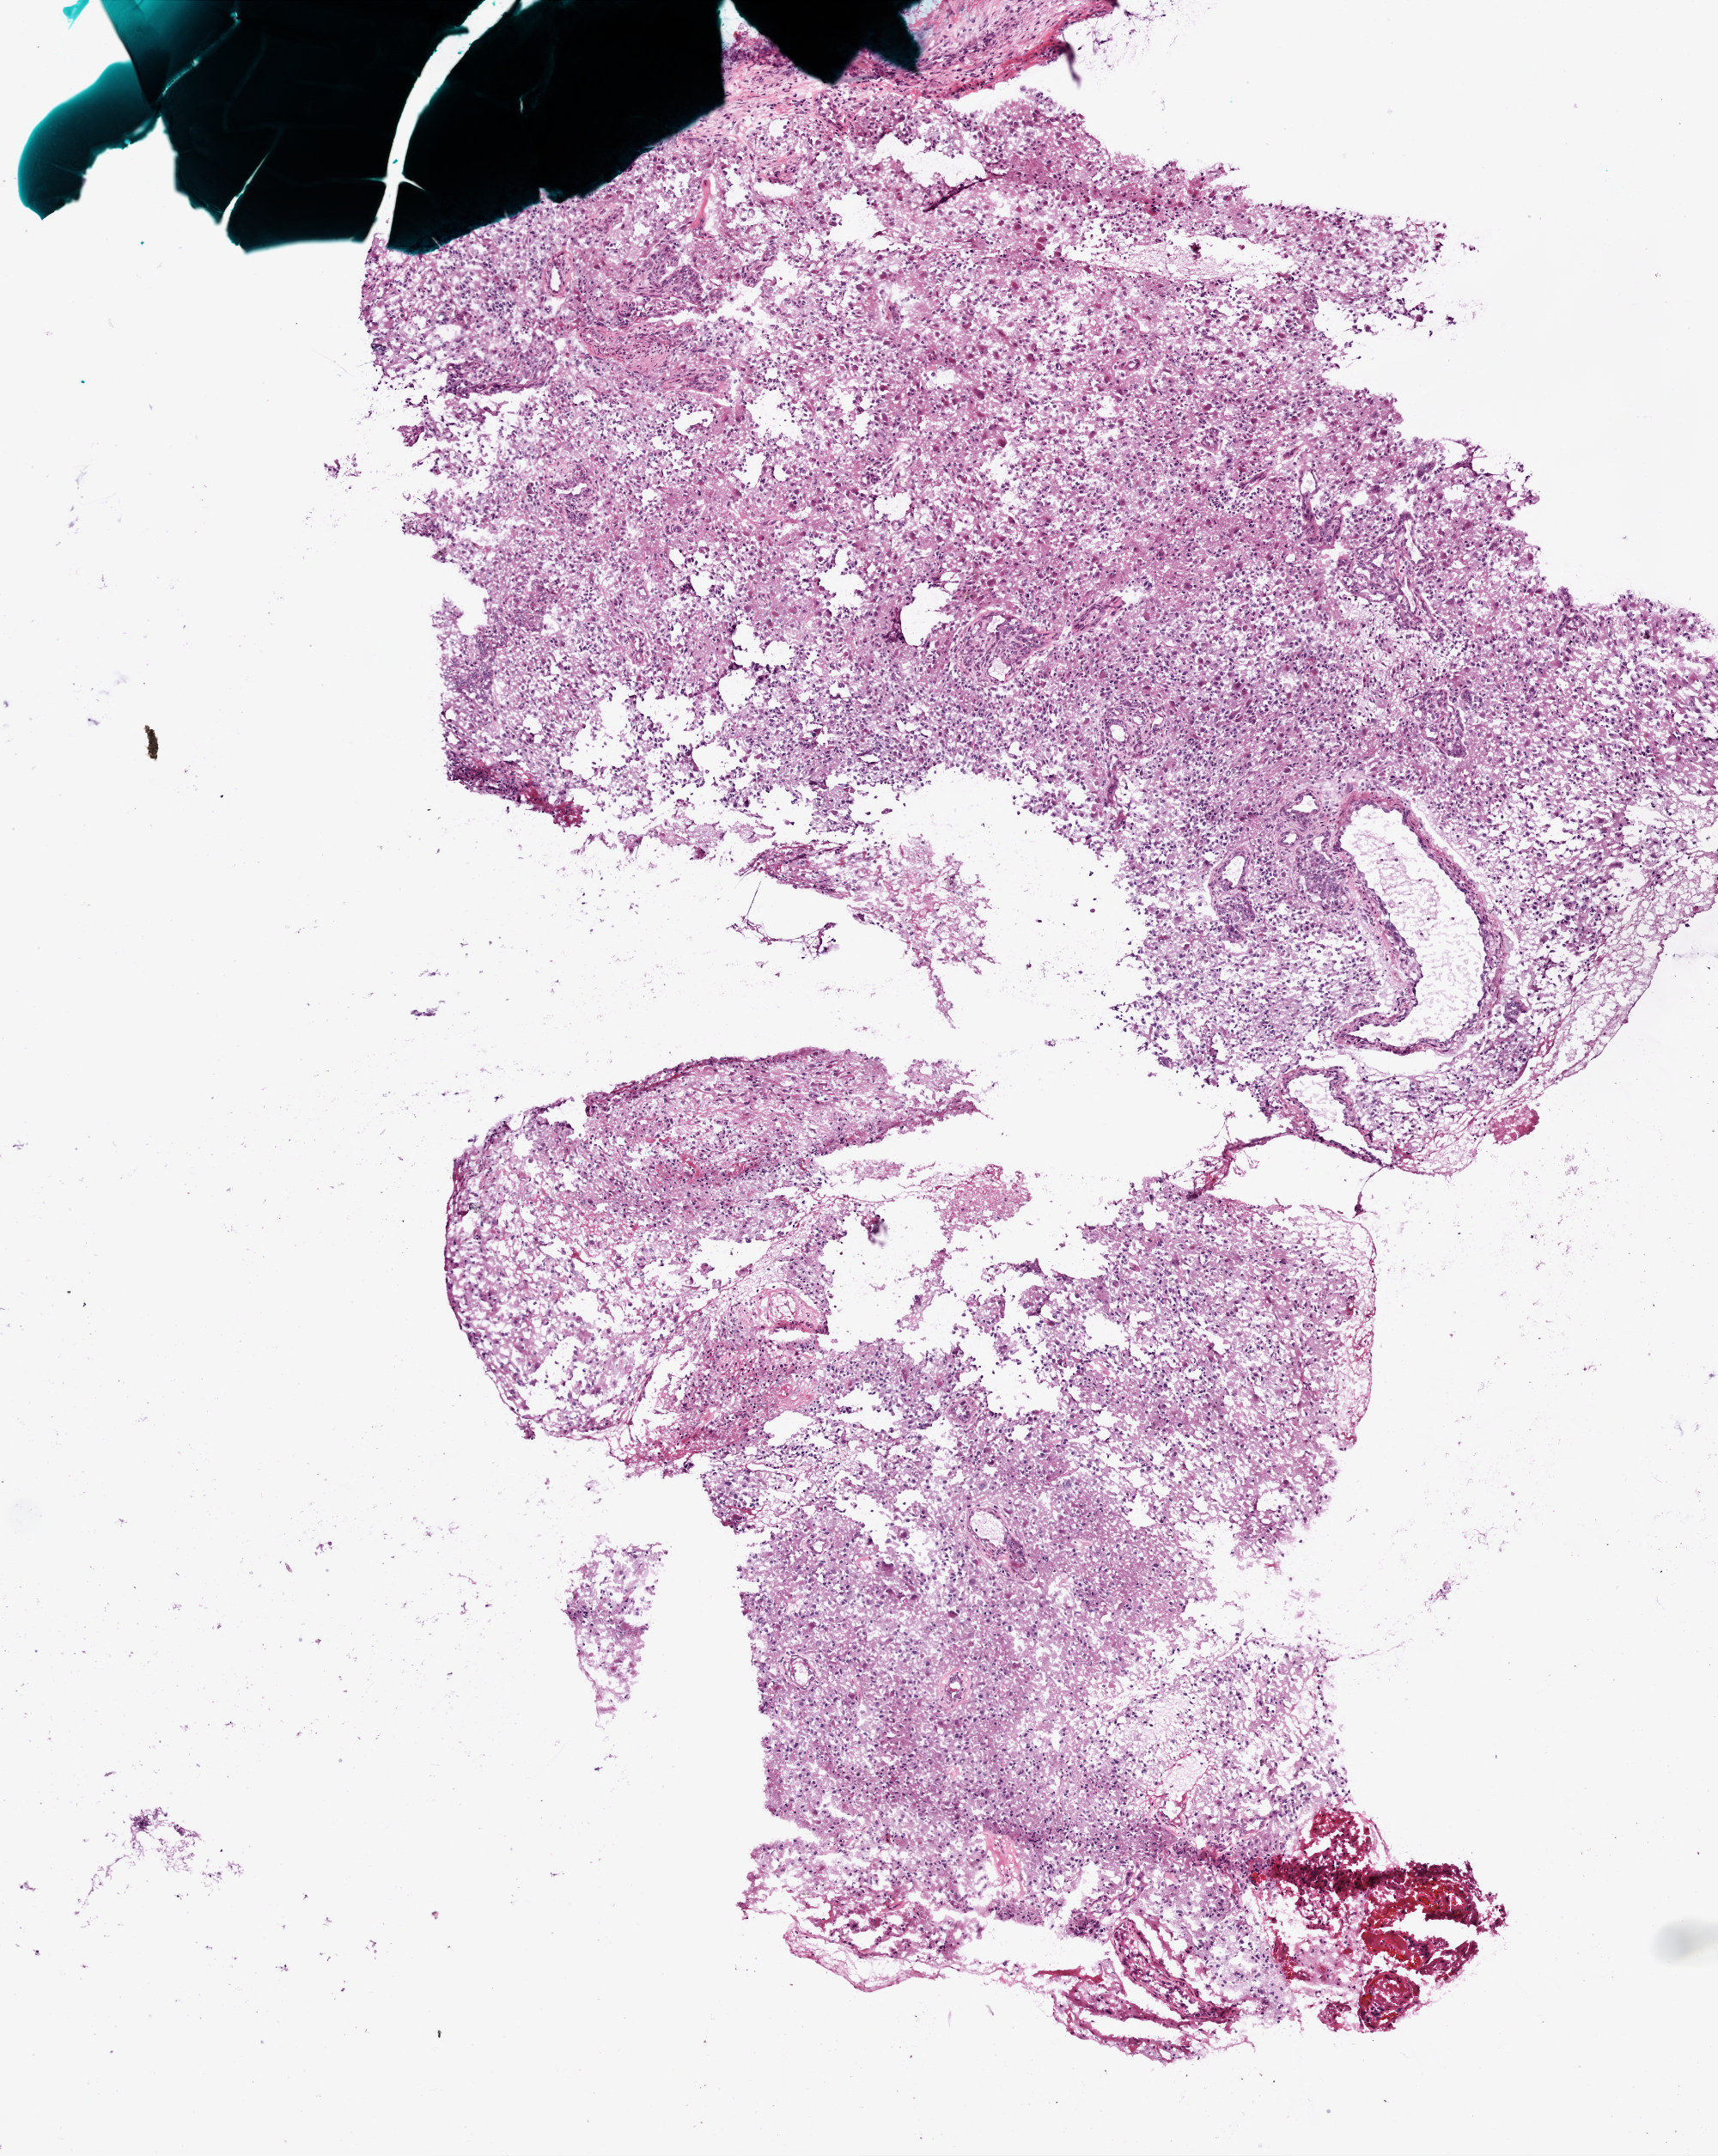
Hematoxylin and eosin (H&E) stained whole-slide image, a low-resolution overview of the entire scanned area, about 4.0 x 5.0 mm (acquisition: 20x scan); frozen section from the bottom of the tissue portion; brain, primary tumour sample. Patient: male, age at initial diagnosis 48 years. Slide review estimates, as recorded: tumour cells 85%, tumour nuclei 80%, normal cells 0%, stromal cells 15%, necrosis 0%.
Histologic diagnosis: Glioblastoma.